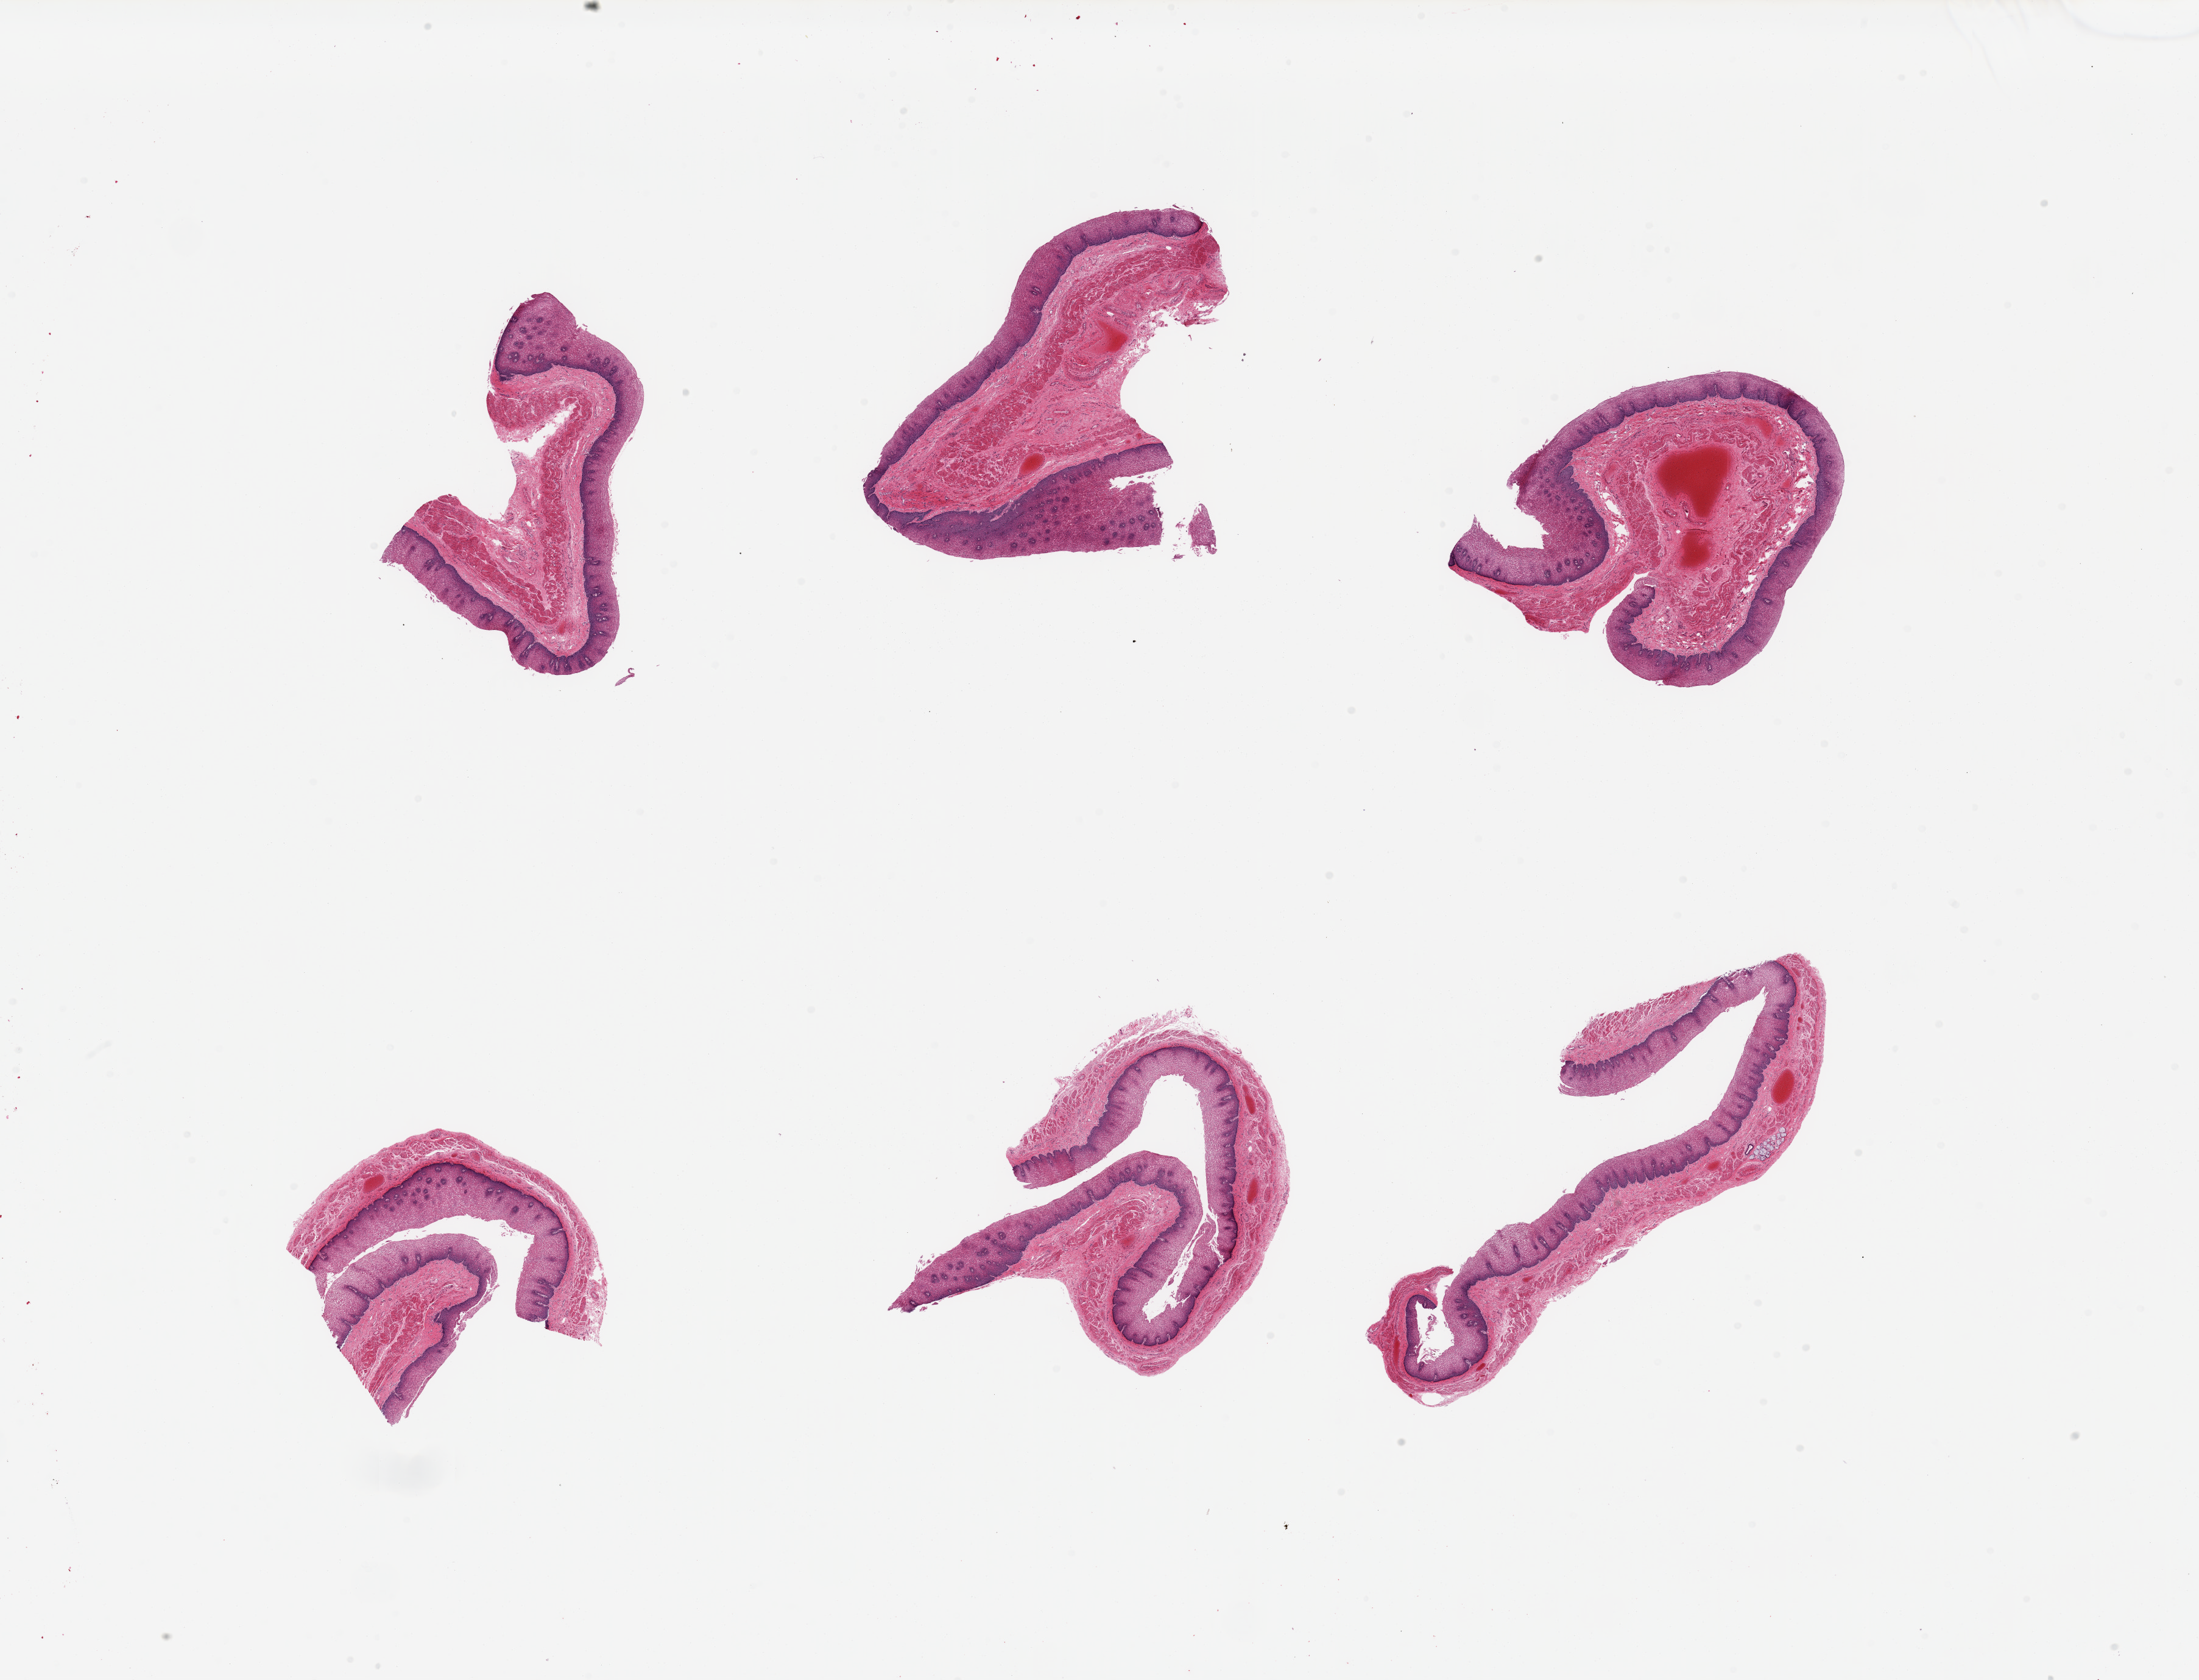
Digitized H&E-stained section, brightfield, shown as a low-resolution overview of the whole scanned area (about 28.5 x 21.8 mm, acquisition: 20x scan); PAXgene-fixed paraffin-embedded (PFPE) section; section of esophageal mucous membrane (target tissue); tissue donor sample. Donor: male.
Pathologist's review note for this sample: 6 pieces; half of the specimens have high mucosal glycogen content.